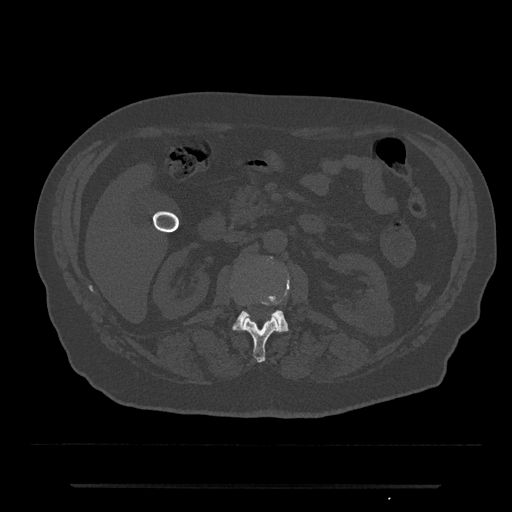
CT including the spine, one axial slice; position 506 of 797 along the scan axis; 120 kVp; bone window (W 1800 / L 400 HU); 0.5 mm slice thickness; 512 × 512 image matrix, field of view 434 × 434 mm. Patient: male, 80 years. From the clinical record (not read from this slice): primary cancer: prostate; vertebrae with lytic lesions (as recorded): L1, T11.
Annotated regions visible in this slice (semi-automatic segmentation, software-assisted and operator-edited):
- L1 vertebra: bounding box <243,303,280,363> (left, top, right, bottom; pixels)
- L2 vertebra: <231,258,290,333>